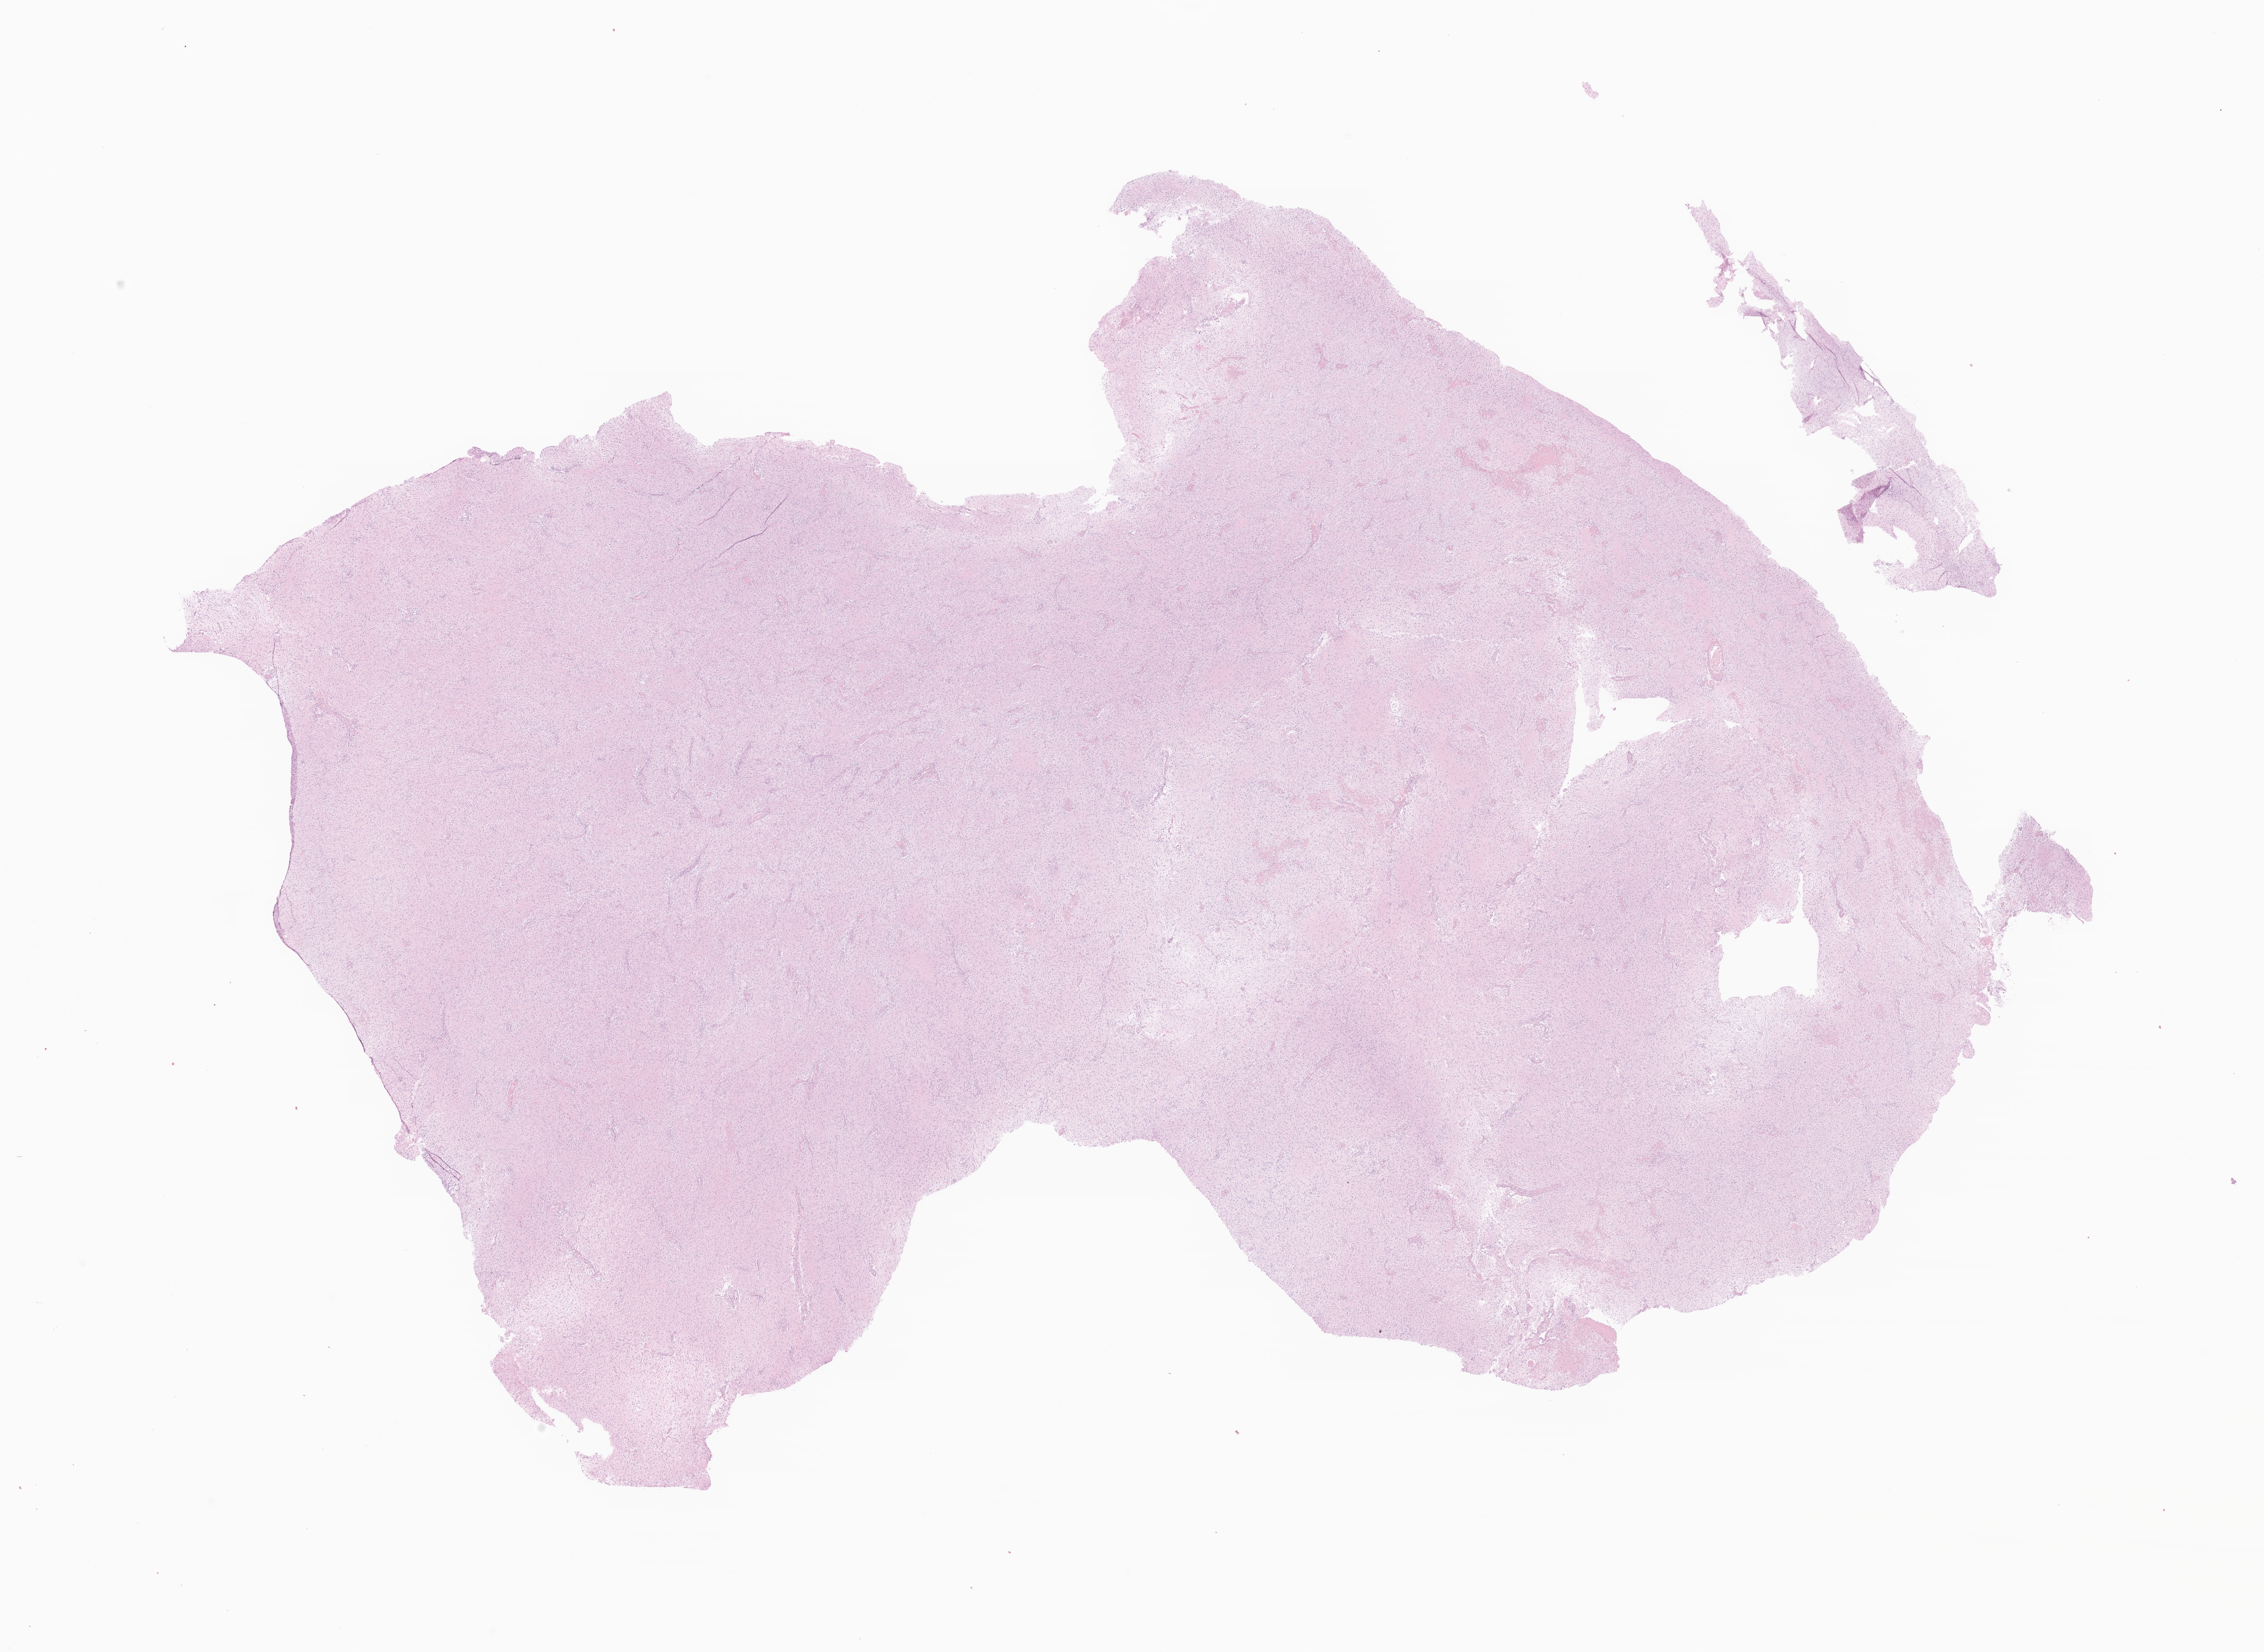
Digitized H&E-stained section of tumor tissue from the brain — low-resolution overview of the scanned area, about 26.4 x 19.3 mm. FFPE section. Patient male; age 128 months (10 years 8 months).
* diagnosis: Pilocytic astrocytoma